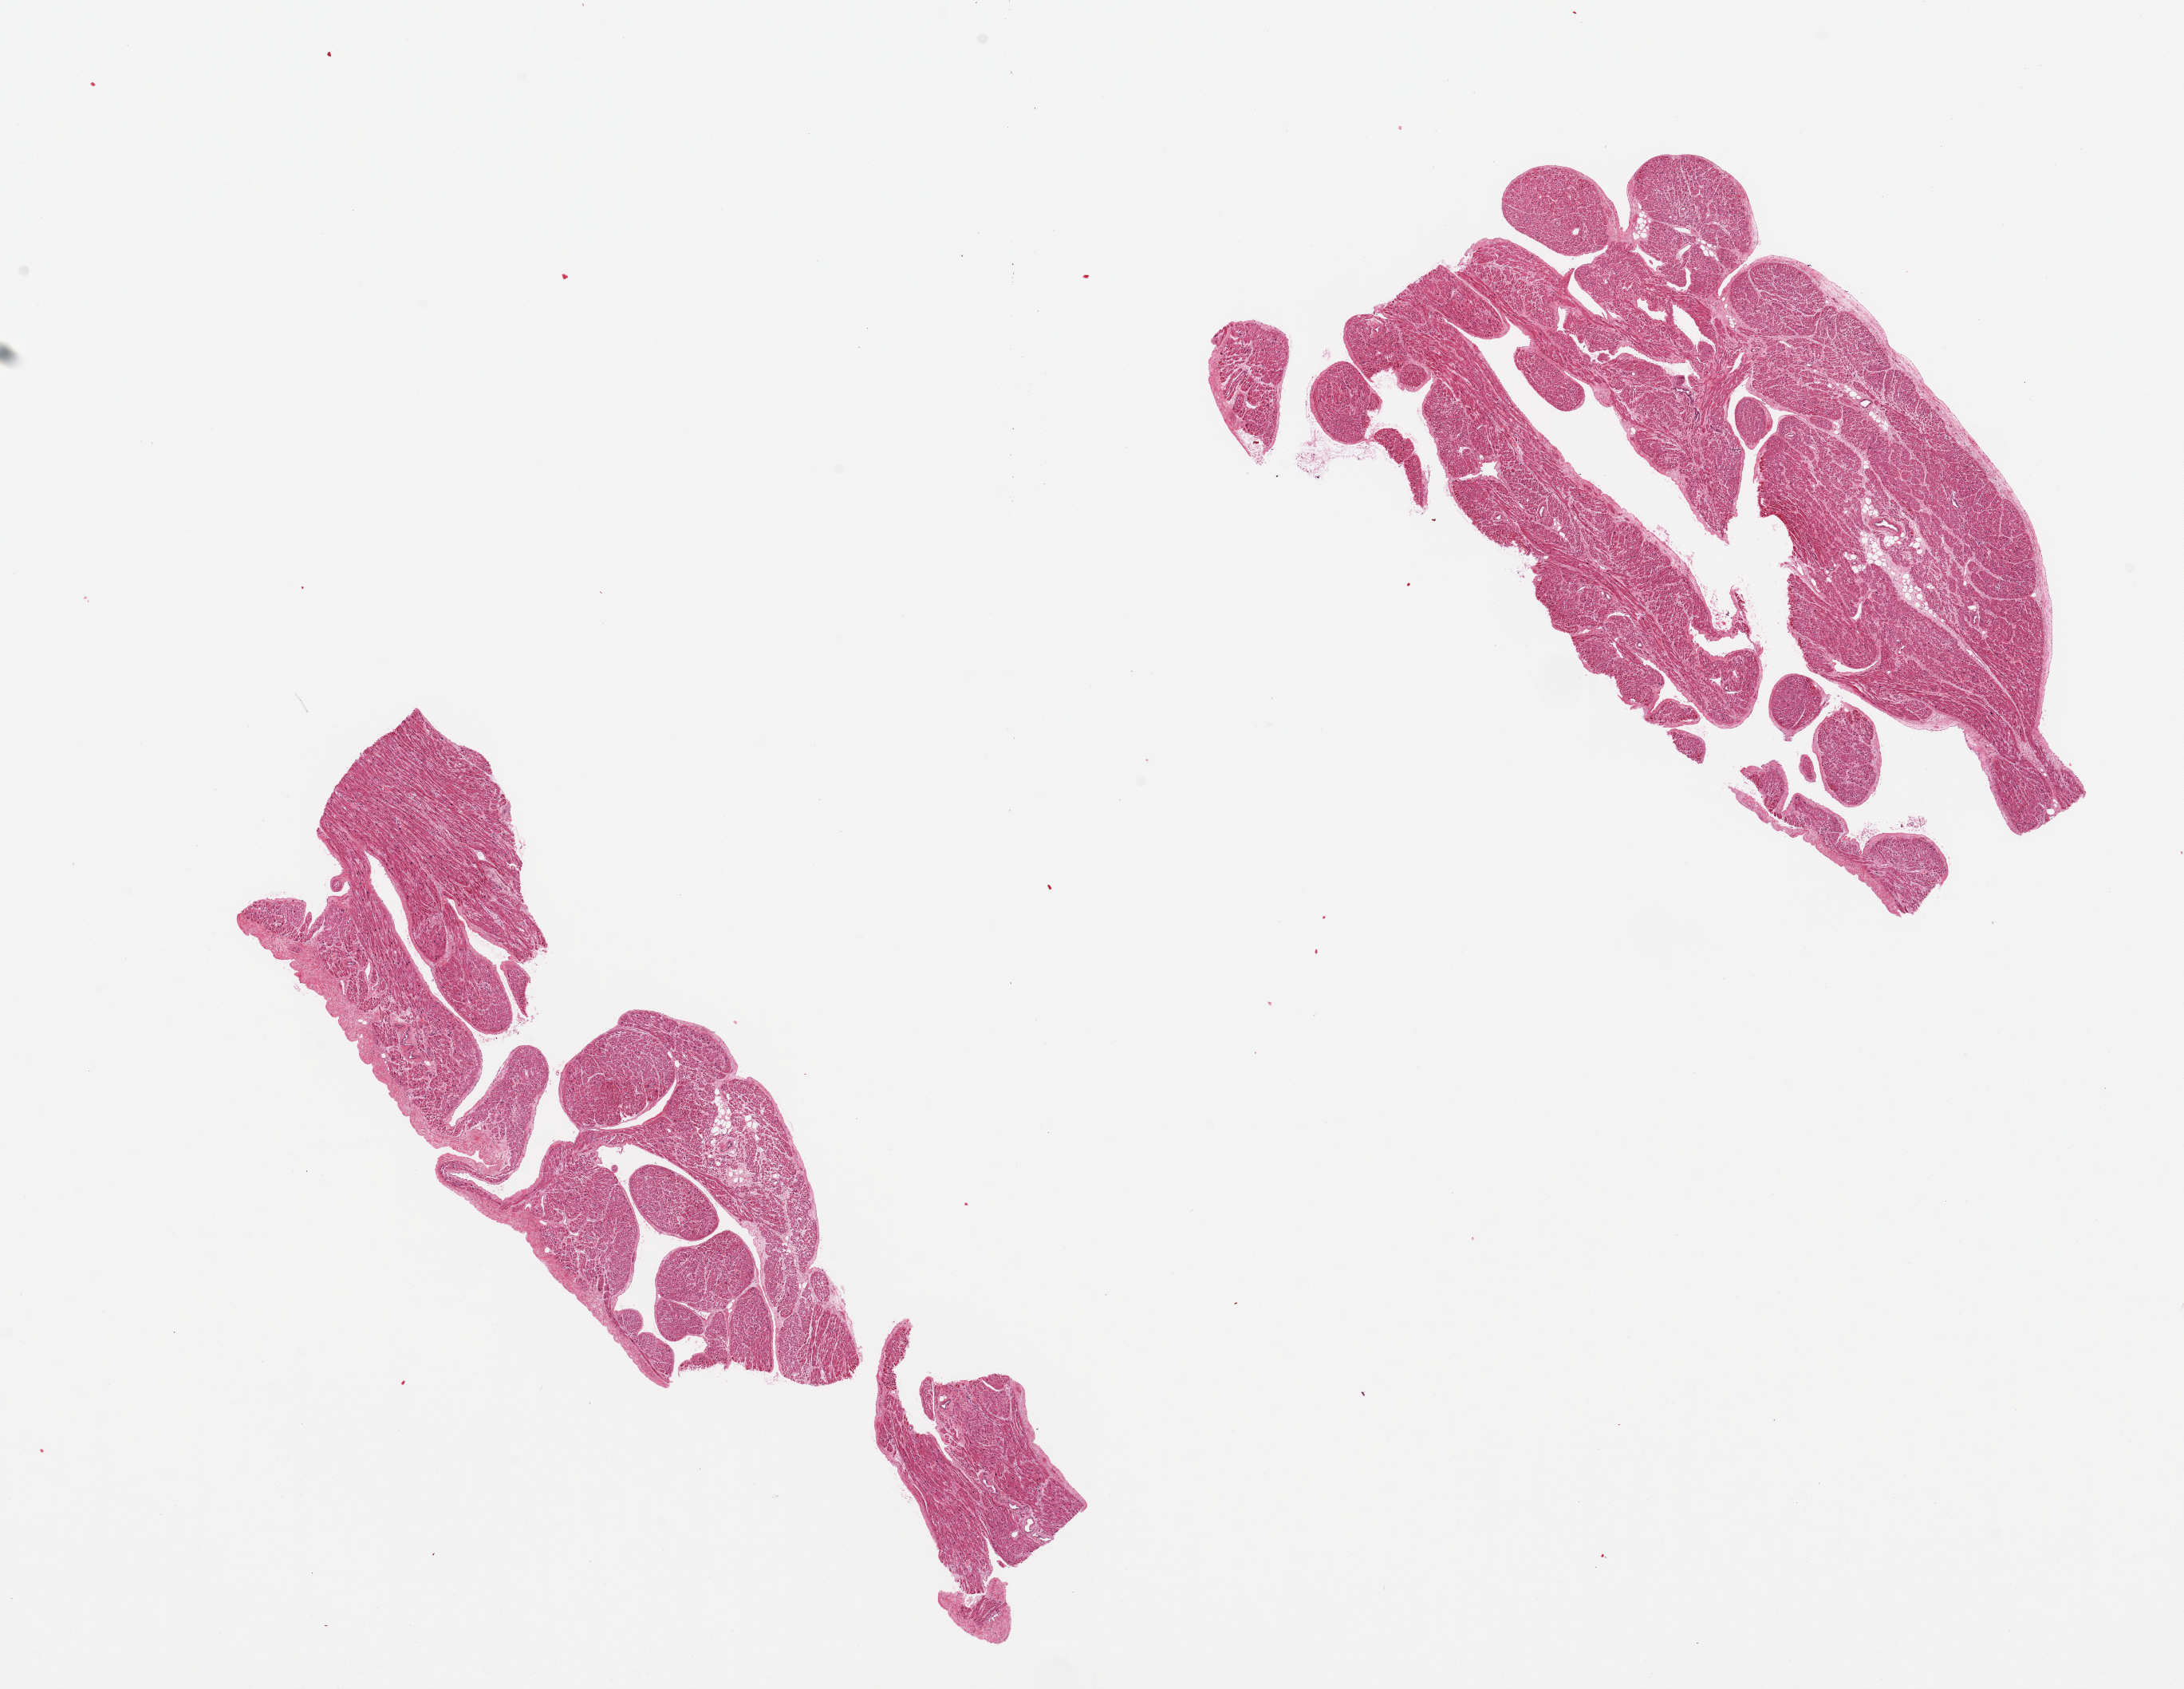
Digitized haematoxylin and eosin-stained section, shown as a low-resolution overview of the whole scanned area (about 21.7 x 16.7 mm). PAXgene-fixed, paraffin-embedded tissue. Target tissue: auricular appendage. Donor tissue sample. Donor: female.
Review note (as recorded): 2 pieces, no abnormalities.